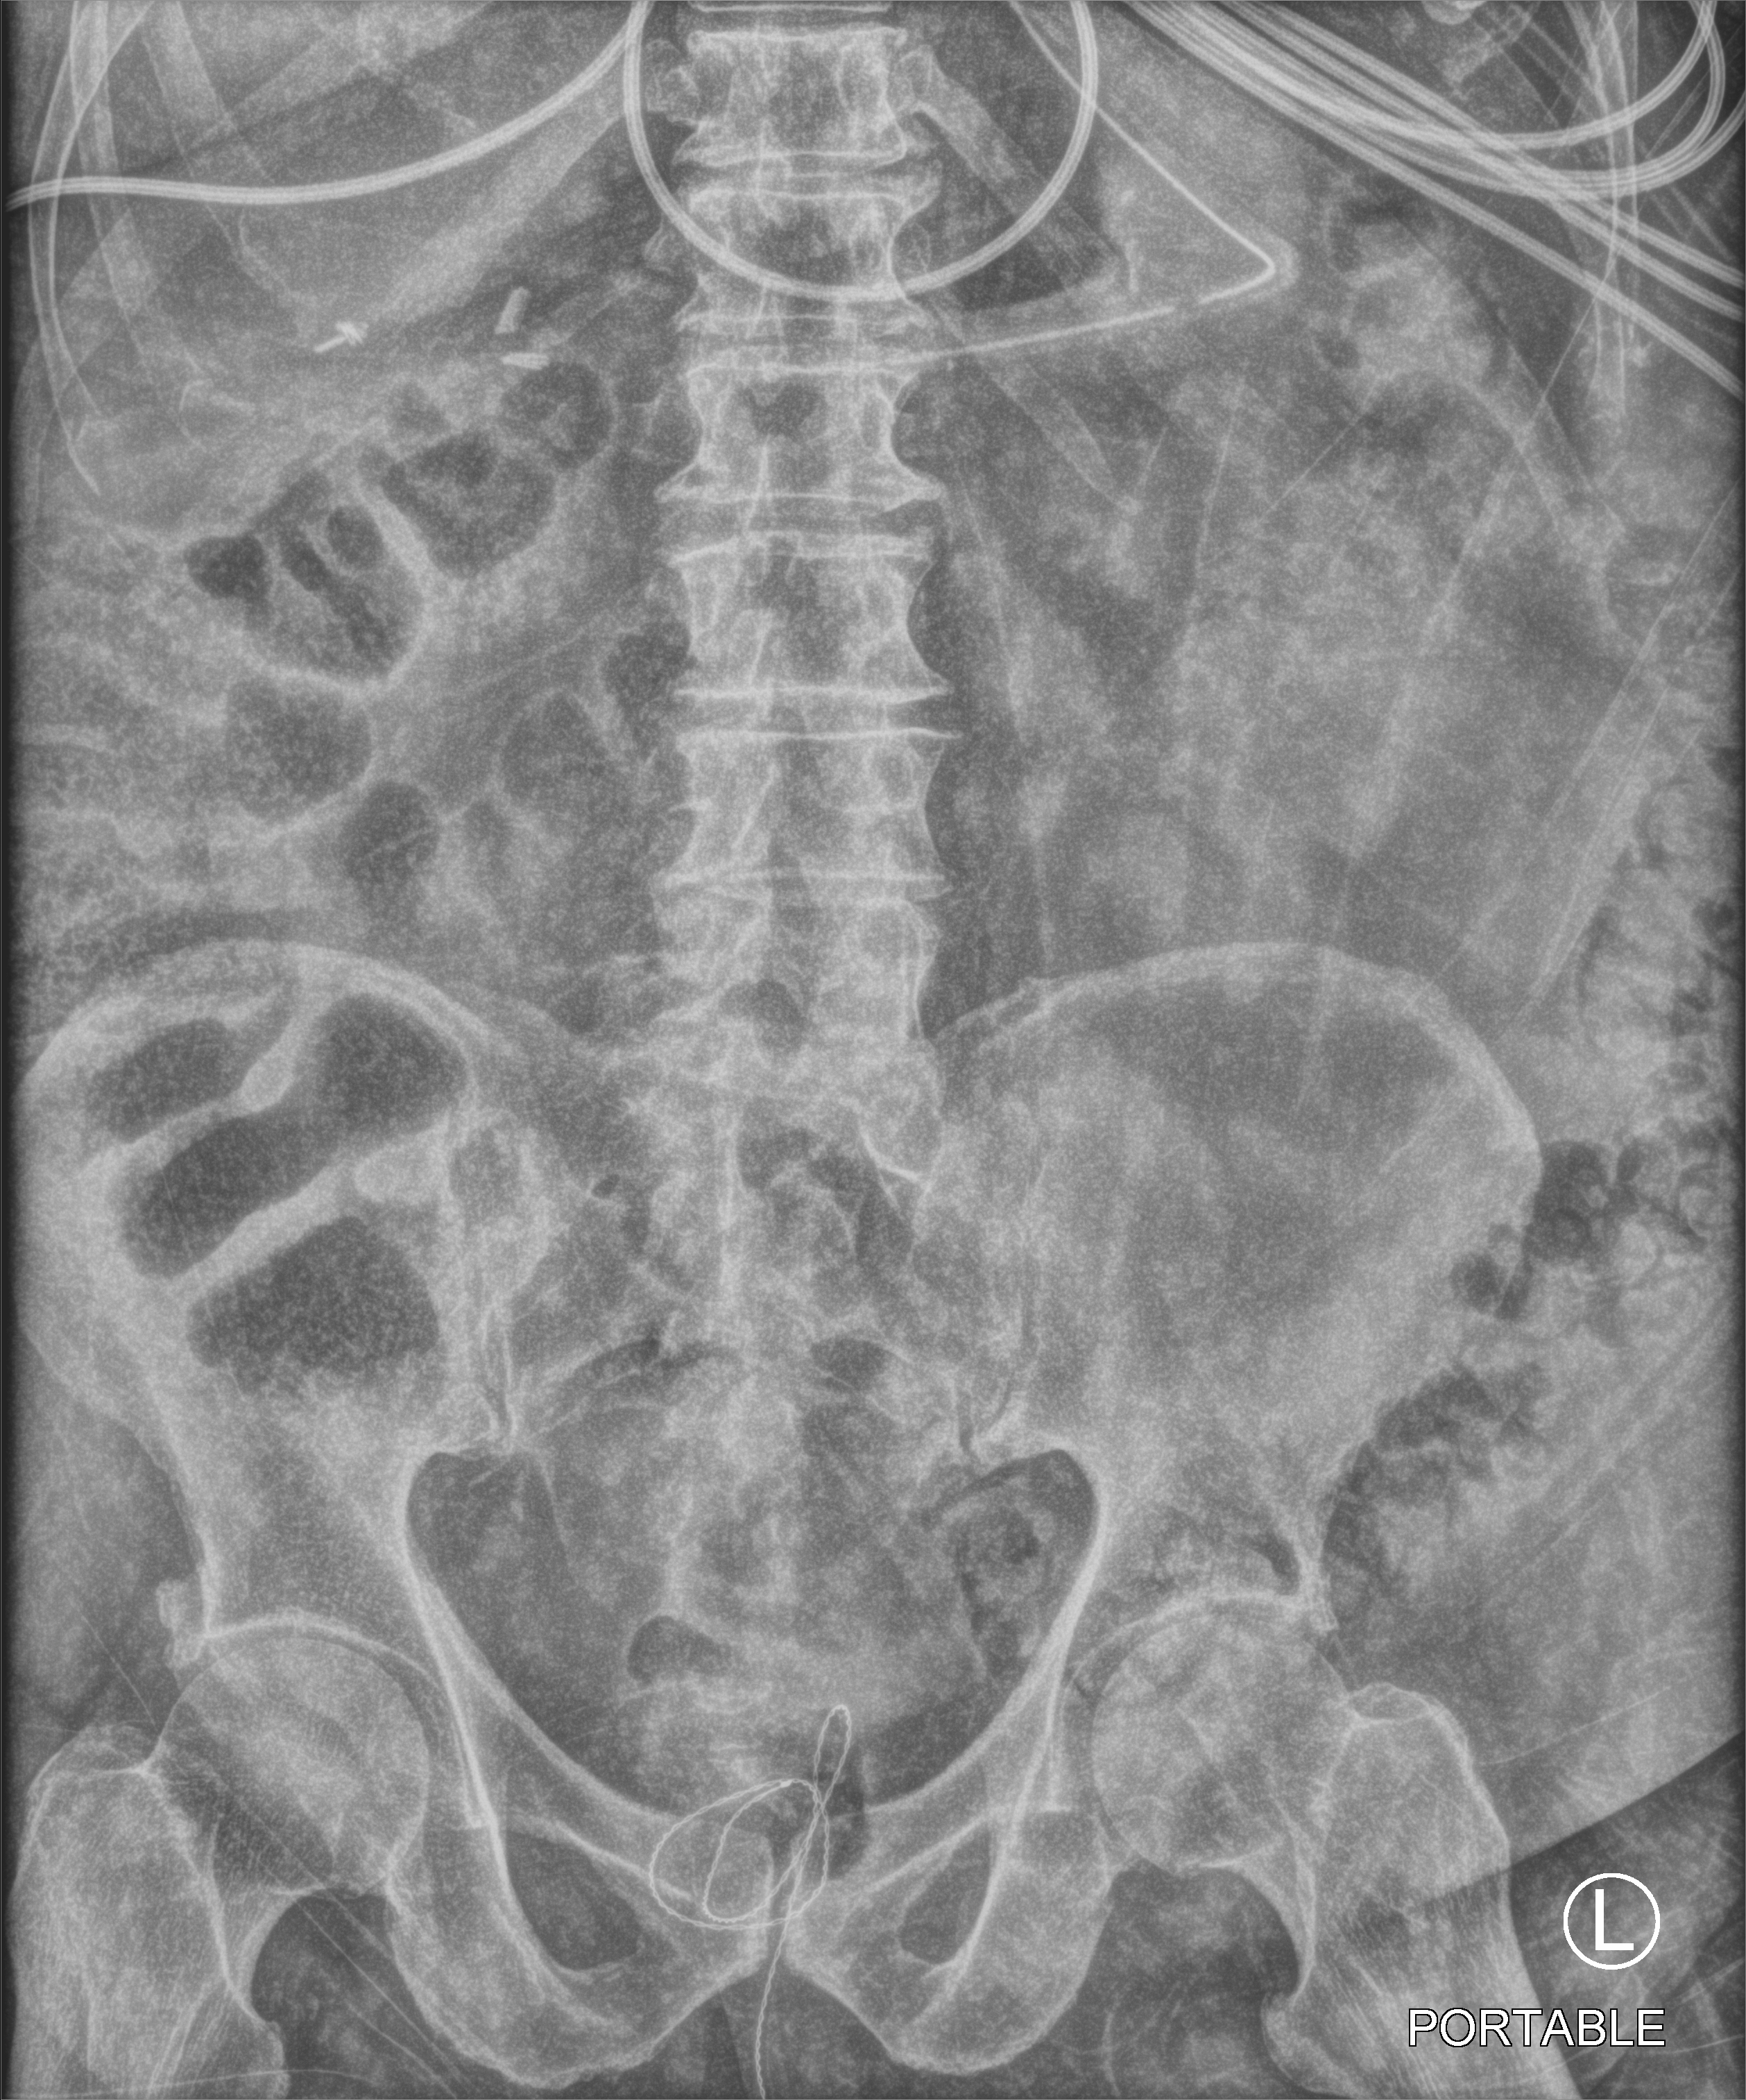
Abdomen X-ray (portable); anteroposterior (AP) projection. Patient hospitalised with COVID-19; male, aged 75–90 years.
Admission-level facts for this patient (not findings on this image; timing relative to this image not recorded):
- mechanically ventilated during this hospital stay: yes
- admitted to intensive care during this hospital stay: yes